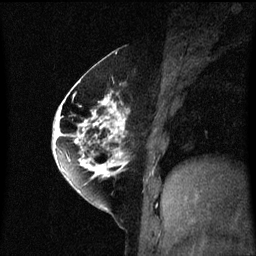
Breast MRI (dynamic contrast-enhanced), one sagittal slice; dynamic contrast-enhanced series, image 2 of 3 at this slice position (ordered by acquisition); 1.5 T; TE 4.2 ms, TR 8.4 ms; 2 mm slice thickness; 256 × 256 image matrix, field of view 200 × 200 mm. Patient: female, 60 years.
Annotated regions visible in this slice (semi-automatically segmented with operator editing):
- analysis volume of interest (the breast-tissue region the enhancement analysis was run in; not a lesion): bounding box (x1, y1, x2, y2) in pixels: (64, 70, 131, 195)
- tumour enhancement mask (voxels above the 70 % enhancement threshold inside the analysis volume of interest): (64, 80, 129, 193)